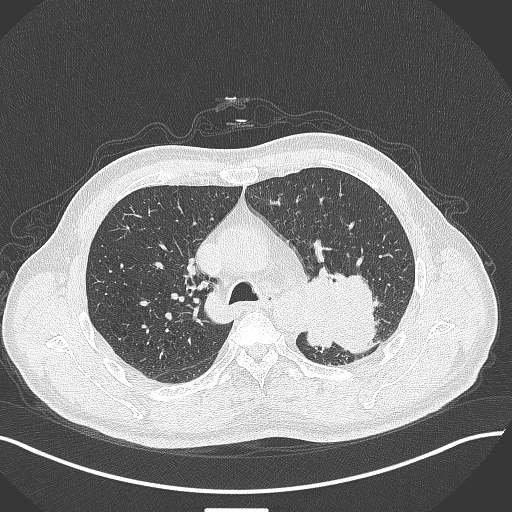
Chest CT, one axial slice. Slice 290 of 429 in the series (ordered by position). Reconstruction kernel B70f. 120 kVp. Lung window (W 1500 / L -600 HU). 512 × 512 image matrix. Patient: male, 55 years. From the clinical record (not read from this slice): clinical TNM (as recorded): T3 N0 M1c; histopathological grade: G3.
Structures marked on this image (rectangle marked by the reading radiologist):
- lung tumour (recorded histology: adenocarcinoma): bounding box <305,267,383,354> (left, top, right, bottom; pixels)